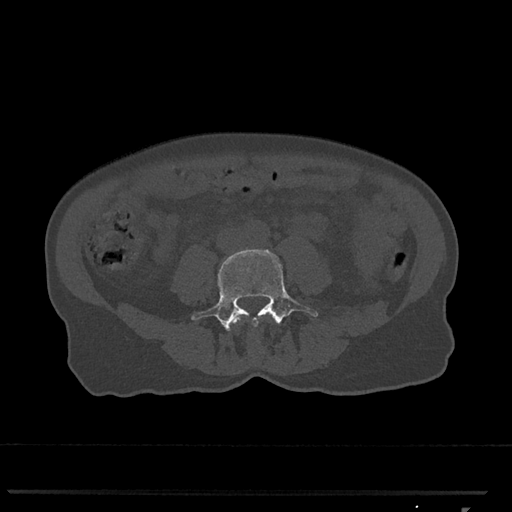
CT including the spine, one axial slice; slice 222 of 793 in the series (ordered by position); bone window (W 1800 / L 400 HU); 512 × 512 image matrix, field of view 380 × 380 mm. Patient: female, 62 years. From the clinical record (not read from this slice): primary cancer: renal.
Annotated regions visible in this slice (semi-automatic segmentation, software-assisted and operator-edited):
- L3 vertebra: box from (x=233, y=314) to (x=269, y=325) px
- L4 vertebra: (x=191, y=249)–(x=318, y=331)